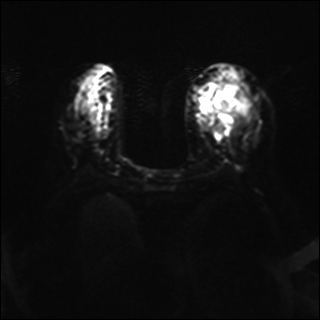
Breast MRI, one axial slice; position 16 of 37 along the scan axis; diffusion-weighted series; image 2 of 4 stored at this slice position (different b-values; order by instance number); 1.5 T; 320 × 320 image matrix, field of view 320 × 320 mm. Female patient.
Annotated regions visible in this slice (expert manual segmentation):
- tumour on diffusion-weighted imaging: box from (x=213, y=81) to (x=249, y=125) px